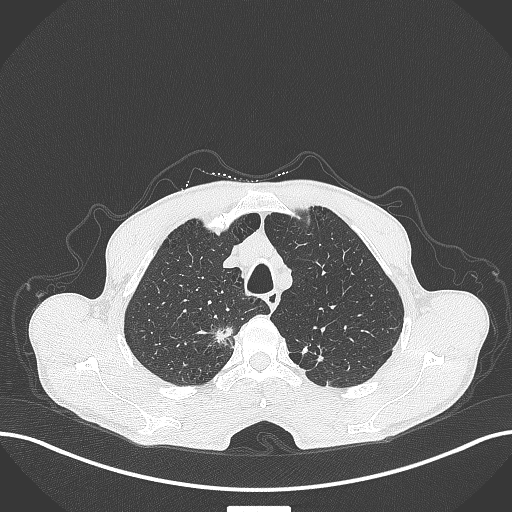
Chest CT, one axial slice. Slice 351 of 445 in the series (ordered by position). Reconstruction kernel B70f. 120 kVp. Lung window (W 1500 / L -600 HU). 1 mm slice thickness. 512 × 512 image matrix, field of view 400 × 400 mm. Male patient, age 70 years. From the clinical record (not read from this slice): clinical TNM (as recorded): T1a N0 M0.
Outlined on this slice (bounding box drawn by a radiologist):
- lung tumour (recorded histology: adenocarcinoma): bounding box (x1, y1, x2, y2) in pixels: (212, 320, 235, 348)